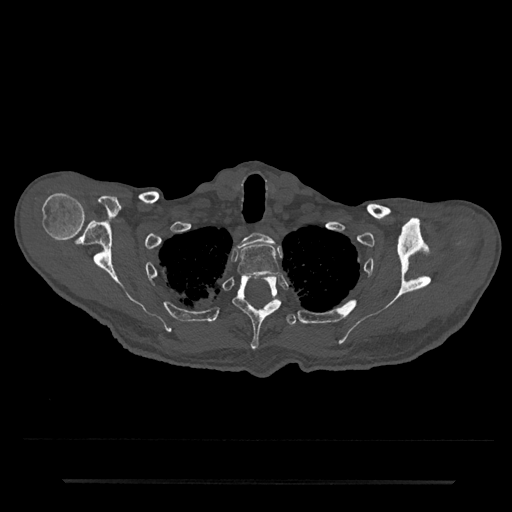
CT including the spine, one axial slice. Position 666 of 797 along the scan axis. Reconstruction kernel Br40s/3. Bone window (W 1800 / L 400 HU). 0.5 mm slice thickness. 512 × 512 image matrix, field of view 427 × 427 mm. Male patient, age 74 years. From the clinical record (not read from this slice): primary cancer: prostate.
Structures marked on this image (semi-automatically segmented with operator editing):
- T1 vertebra: bounding box <237,233,274,249> (left, top, right, bottom; pixels)
- T2 vertebra: <237,244,280,276>
- T3 vertebra: <233,275,282,350>
- T4 vertebra: <222,314,297,327>